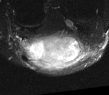
MRI of an extremity soft-tissue mass, one axial slice. Position 16 of 52 along the scan axis. T2-weighted fat-saturated. MR volume resampled by the dataset authors to the PET/CT grid (not the native acquisition matrix). 3.27 mm slice thickness. 109 × 95 image matrix, field of view 106 × 93 mm. Male patient. Case-level facts recorded for this patient, not image findings: histological type: synovial sarcoma; site of the primary tumour: left poplietal fossa.
Outlined on this slice (expert contour drawn on MRI and transferred to this co-registered scan by the dataset authors):
- gross tumour volume (mass): bounding box [x1, y1, x2, y2] px = [21, 31, 84, 70]